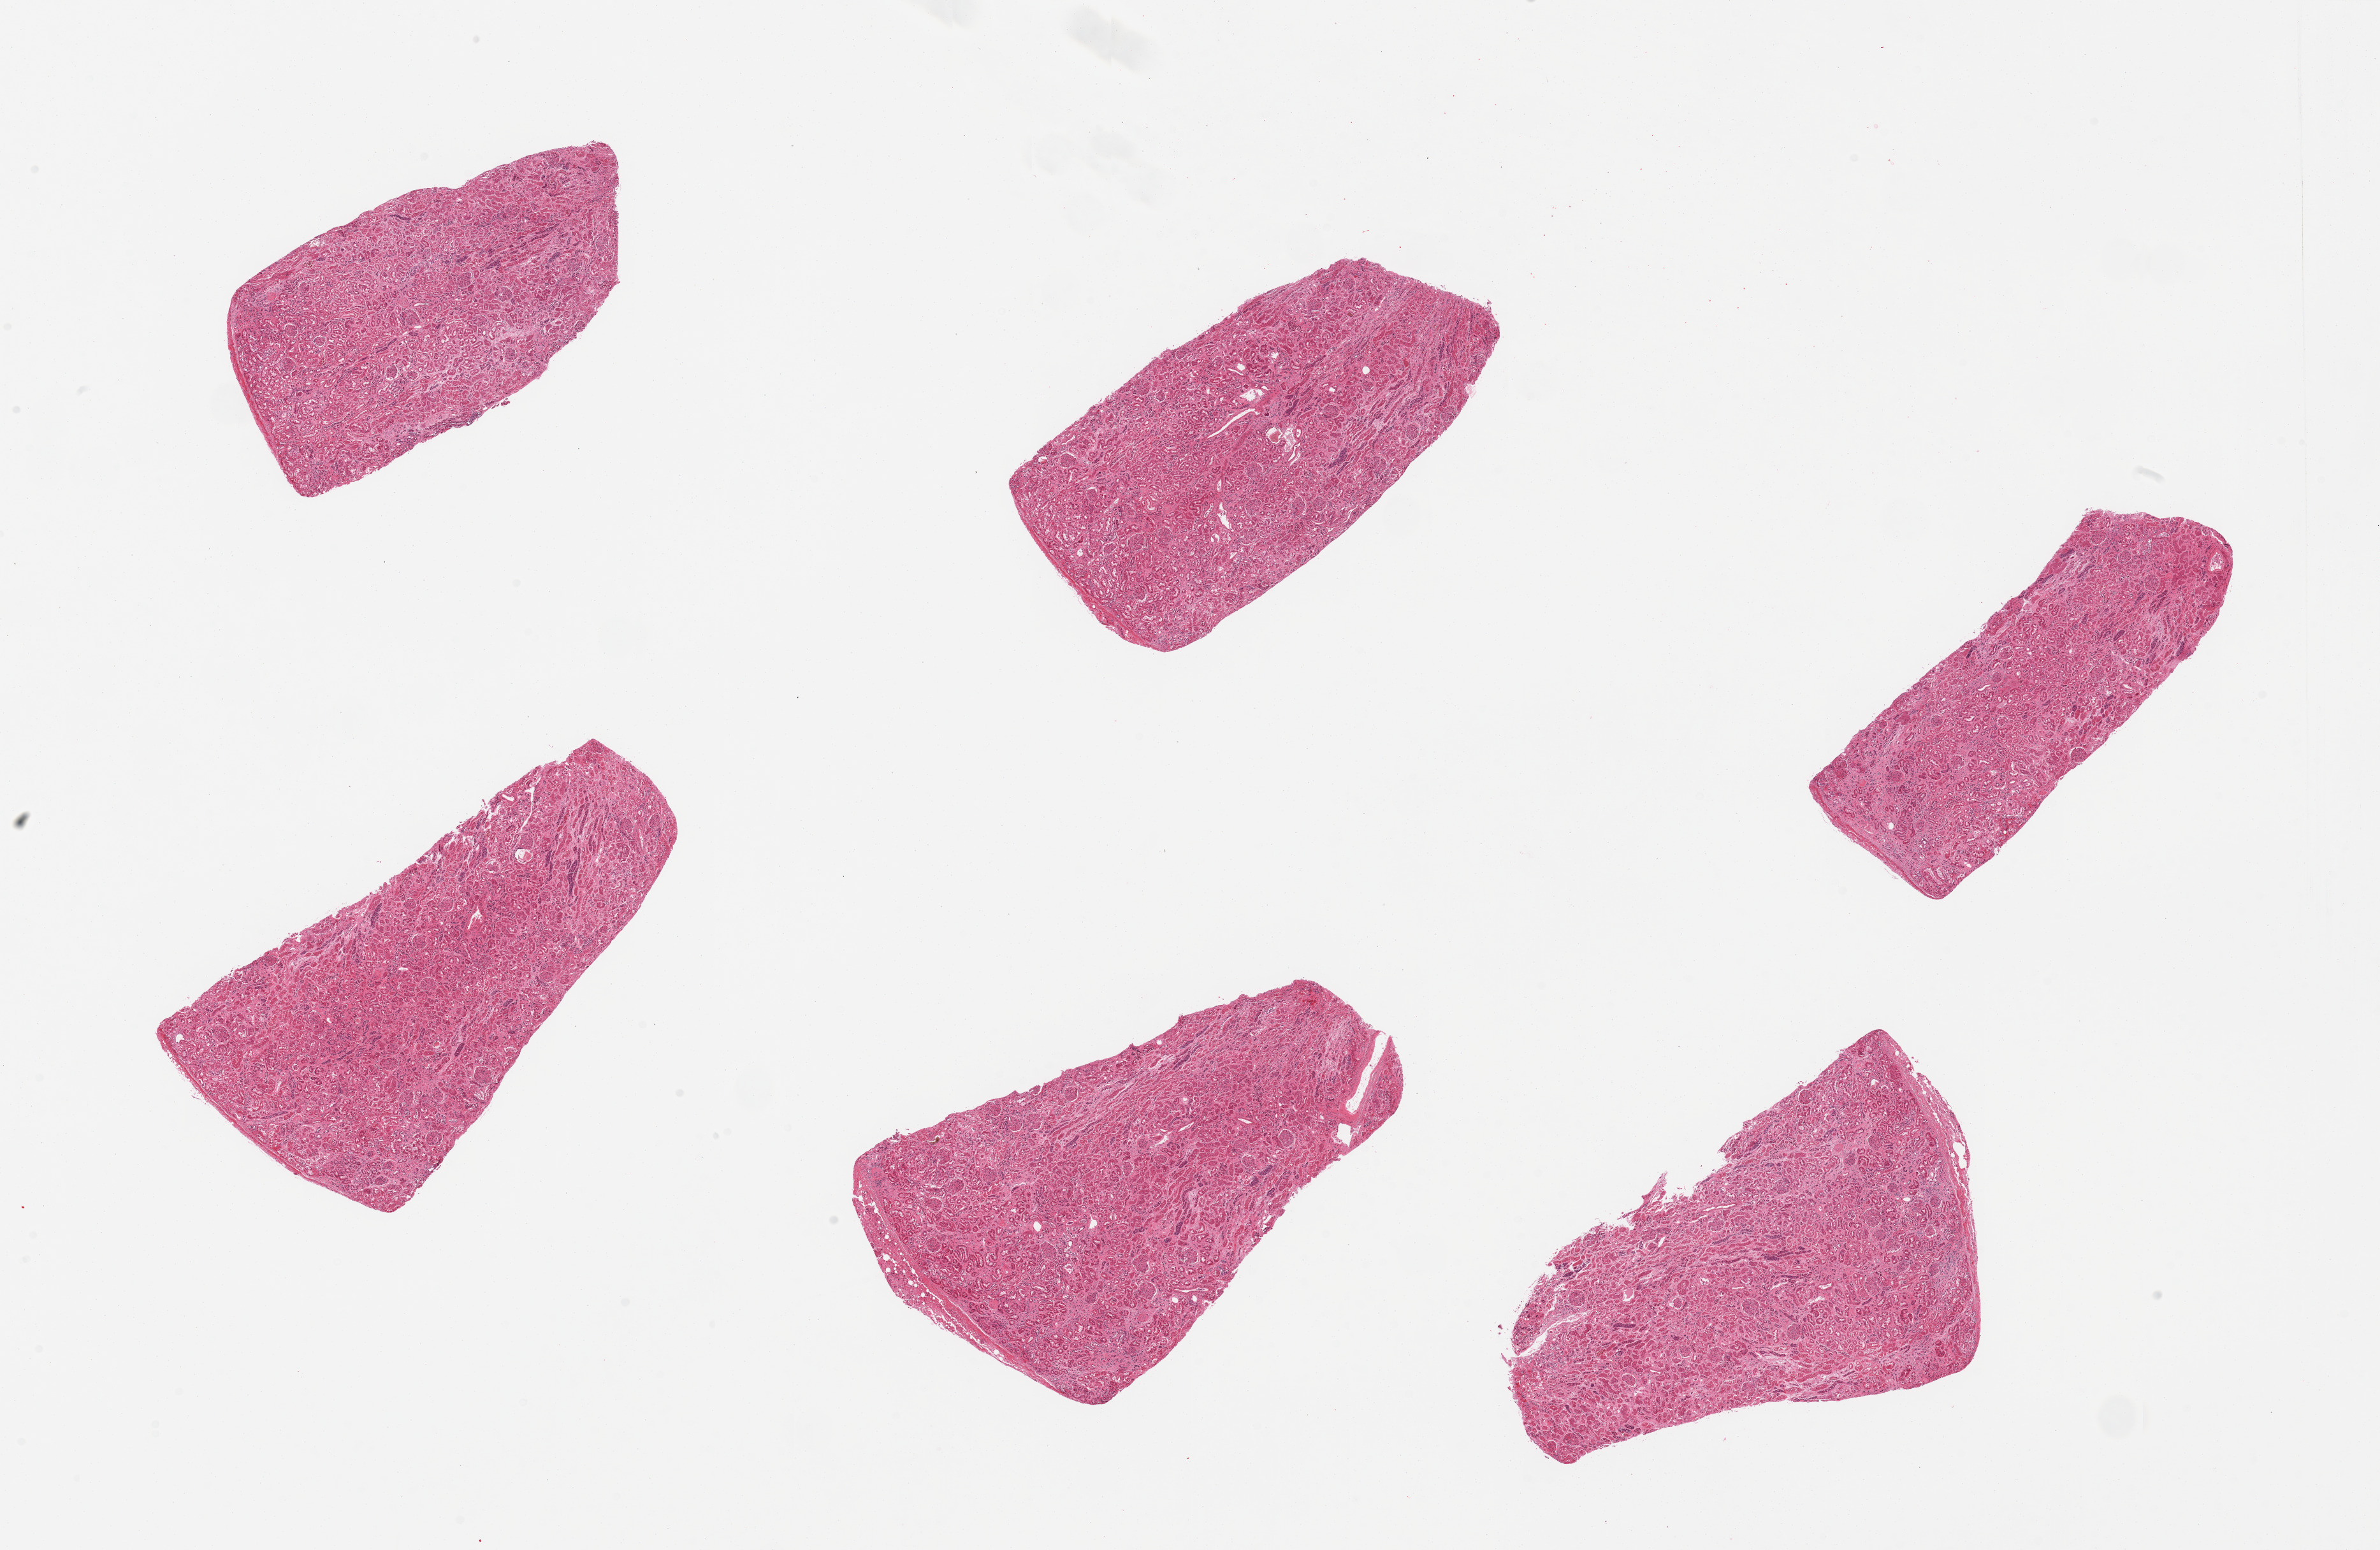
Haematoxylin and eosin whole-slide image, shown as a low-resolution overview of the whole scanned area (about 29.5 x 19.2 mm, slide scanned at 20x), PAXgene-fixed paraffin-embedded (PFPE) section, sampled site (target tissue): renal cortex, donor tissue sample. Donor sex: female.
Reviewer comment on this tissue sample: 6 pieces, glomeruli in all sections, some sclerotic, tubules very autolyzed.